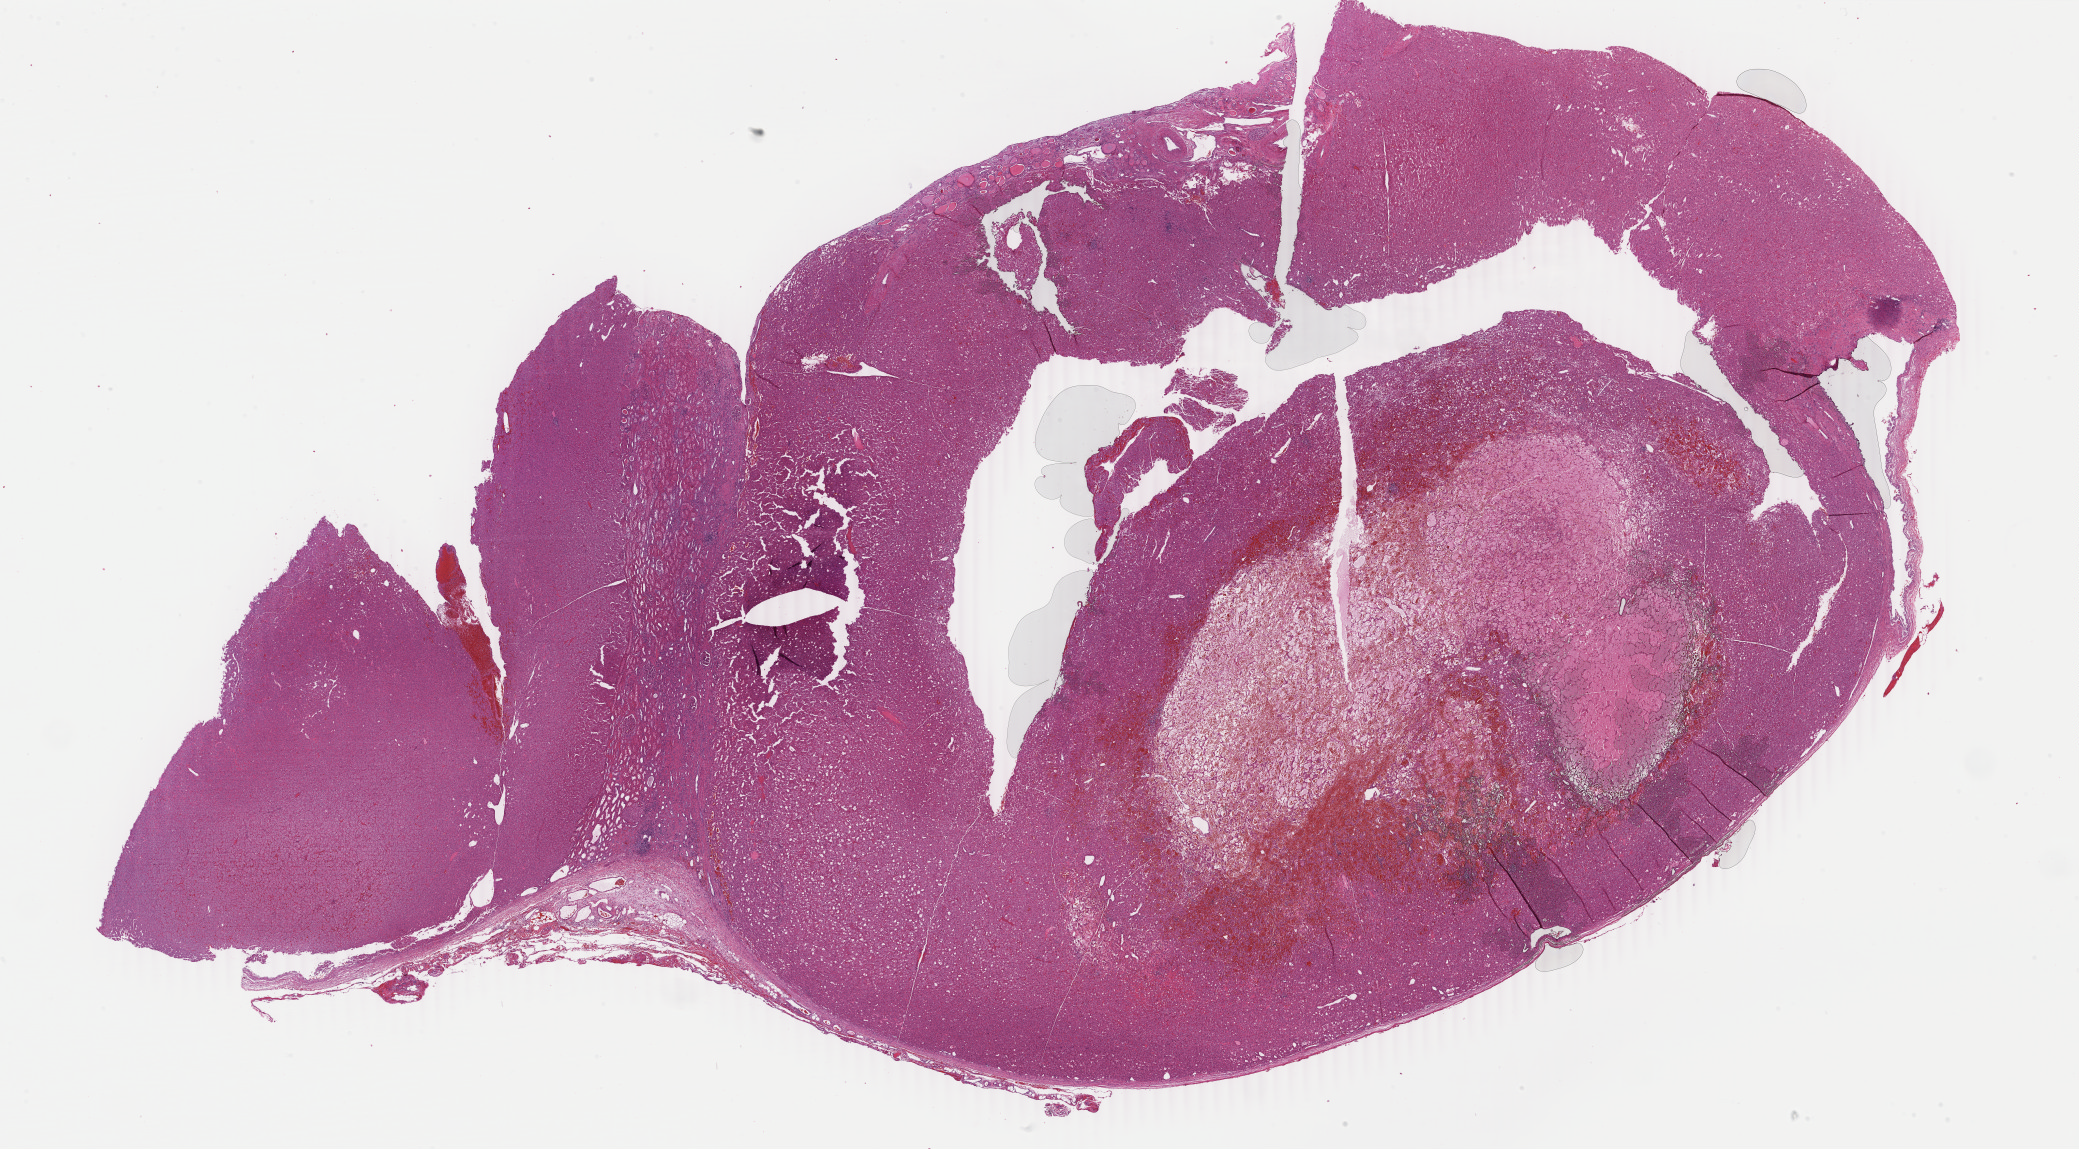
Digitized H&E tissue section (whole slide) — whole scanned area (about 33.1 x 18.3 mm, from a 40x scan) shown as a low-resolution overview; formalin-fixed paraffin-embedded (FFPE) diagnostic section; kidney, primary tumour sample. Female patient; age at initial diagnosis 61 years.
- TNM: T1b NX MX
- histologic diagnosis: Renal cell carcinoma, chromophobe type
- AJCC pathologic stage: I (7th edition)